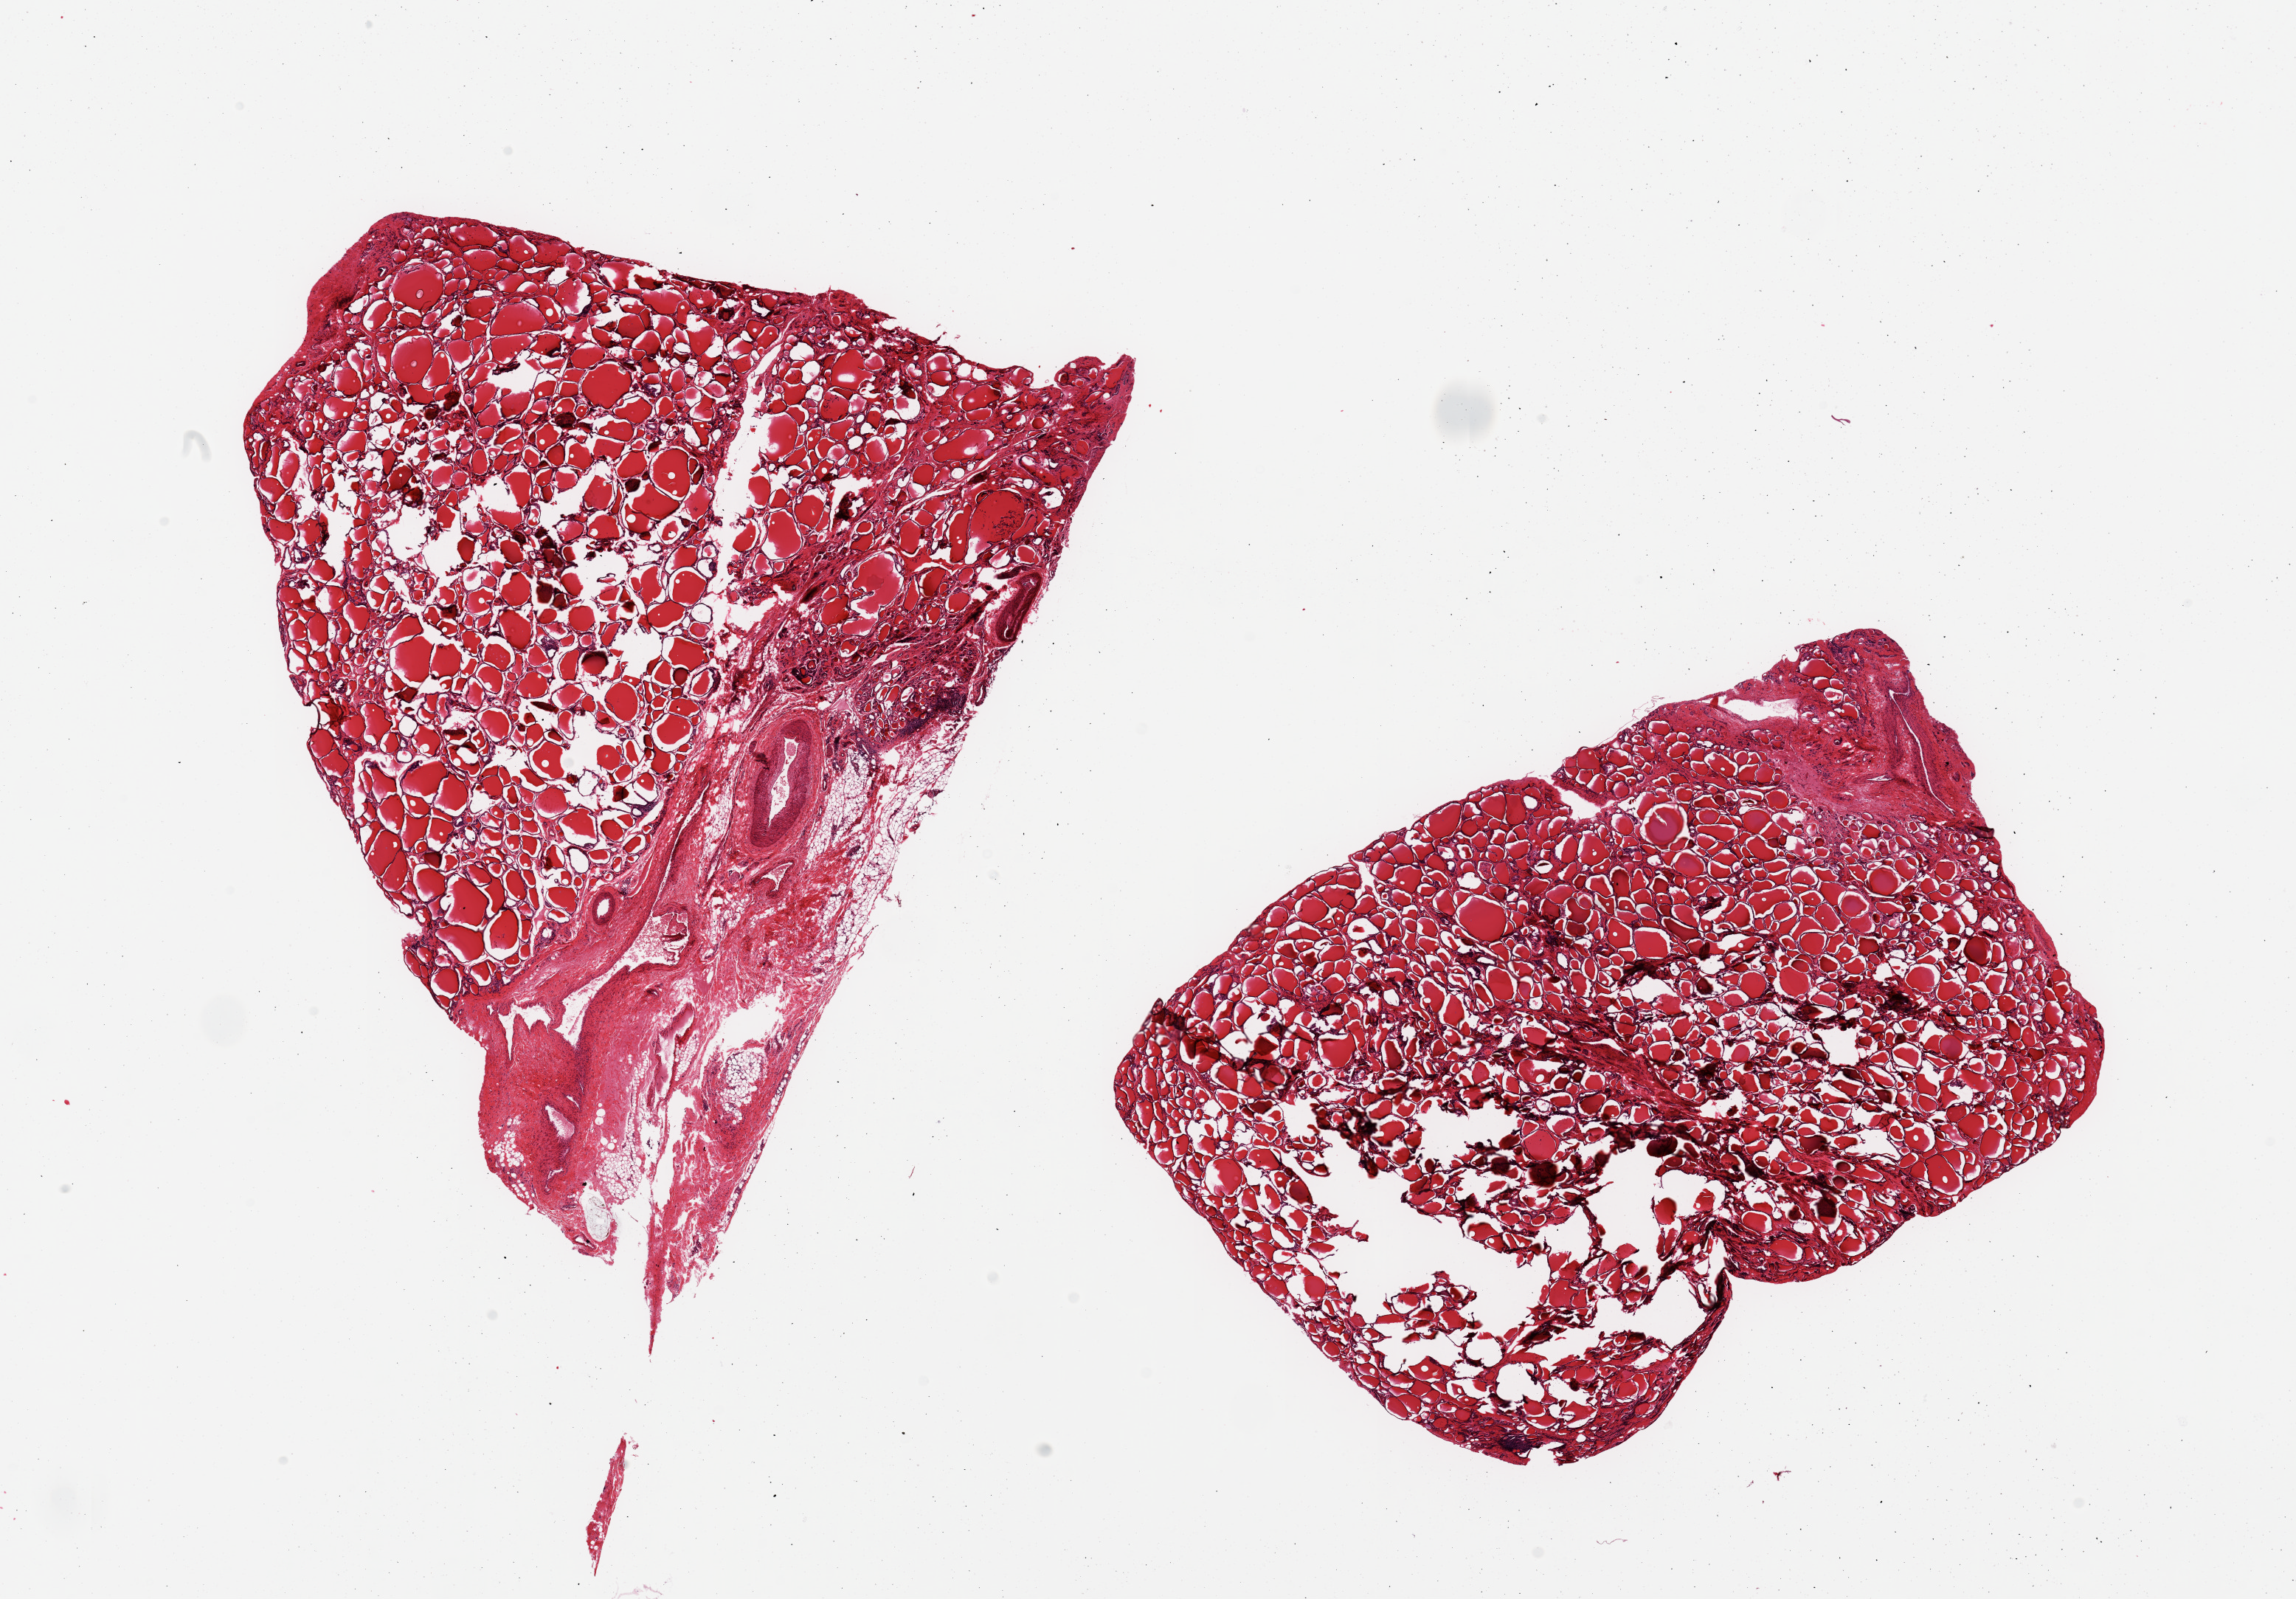
Digitized haematoxylin and eosin-stained section — whole scanned area (about 24.6 x 17.1 mm) shown as a low-resolution overview; PAXgene-fixed, paraffin-embedded tissue; section of thyroid (target tissue); tissue donor sample.
Pathologist's review note for this sample: 2 pieces, ~20 adherent fat, no abnormalities.